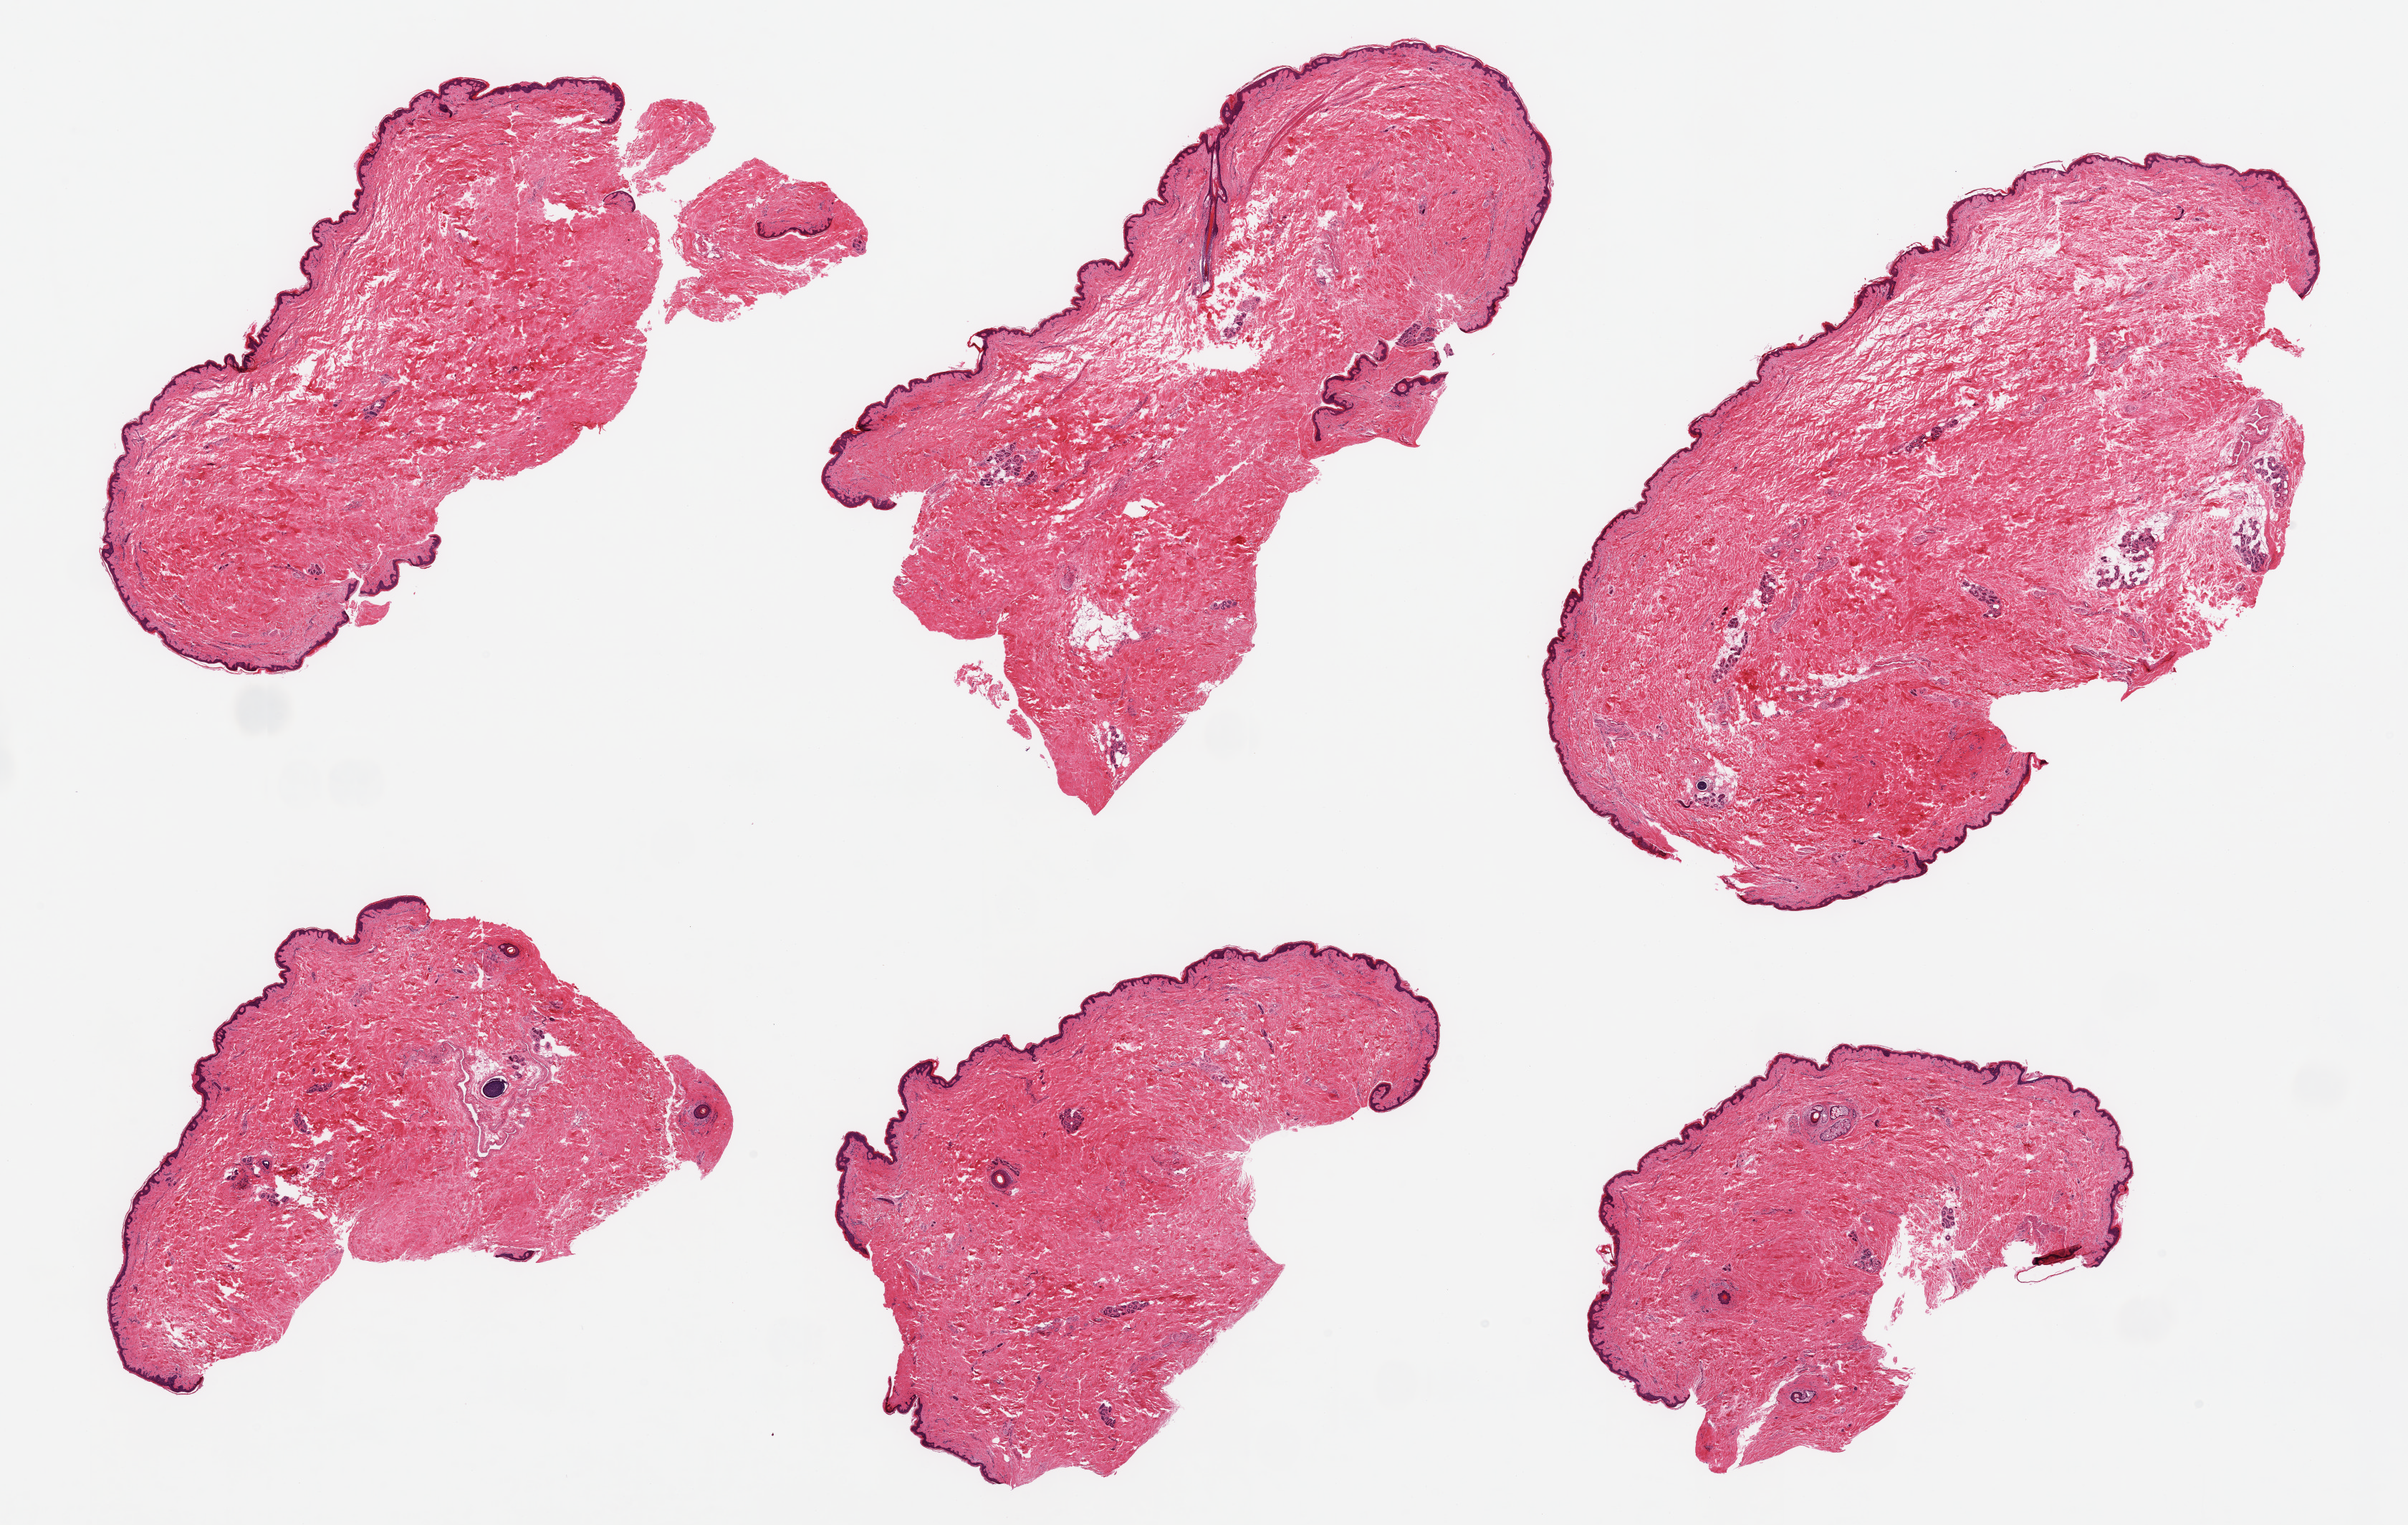
Whole-slide image, haematoxylin and eosin stain, brightfield — a low-resolution overview of the entire scanned area, about 26.6 x 16.8 mm (slide scanned at 20x), PAXgene-fixed paraffin-embedded (PFPE) section, sampled site (target tissue): skin of suprapubic region, donor tissue sample. Donor: female.
* pathologist's review note for this sample: 6 pieces; well trimmed; minimal dermal fat